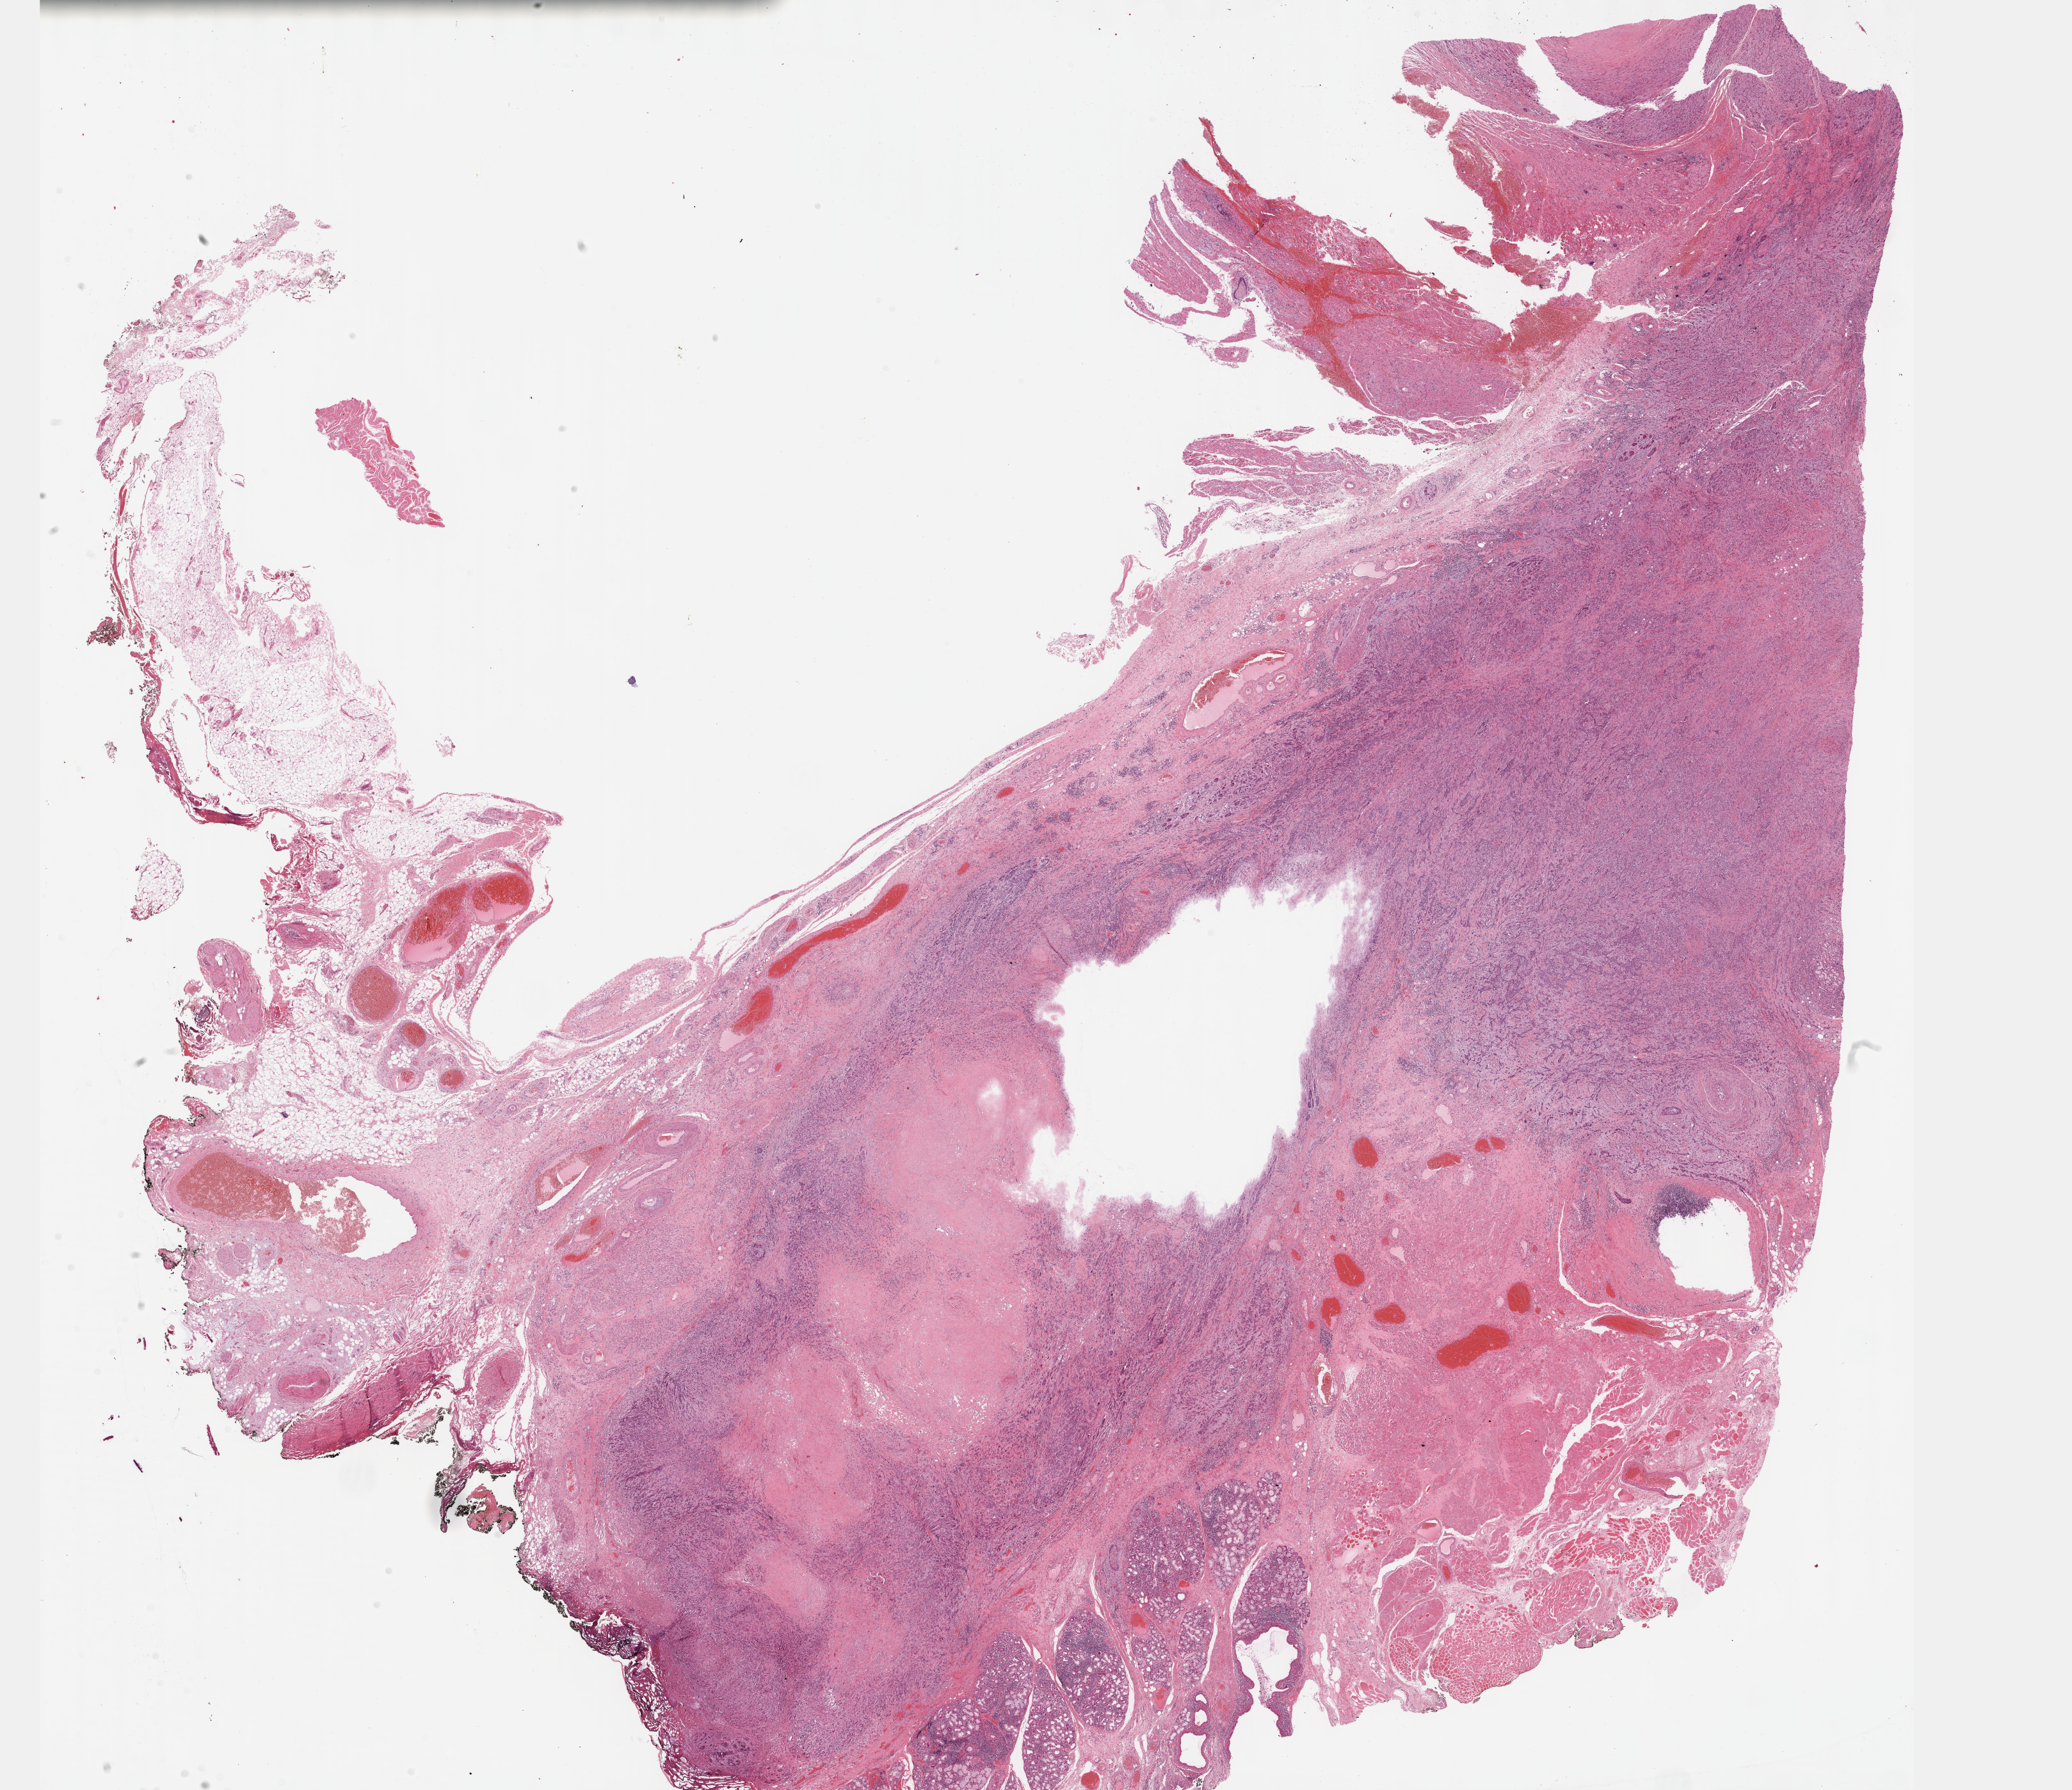
Digitized Hematoxylin and eosin (H&E) stained tissue section (whole slide) — shown as a low-resolution overview of the whole scanned area (about 26.2 x 22.6 mm, acquisition: 40x scan). FFPE section. Primary tumour sample from the head and neck. Male, age 71 years at initial diagnosis. Histologic grade: G3 (poorly differentiated).
AJCC pathologic stage: IVA (7th edition). TNM: T4 N2b M0. Pathologic diagnosis: Squamous cell carcinoma, NOS (cheek mucosa). Laterality: right.